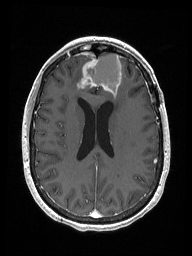
Brain MRI from a brain-tumour surgery series, one axial slice. Slice 69 of 192 in the series (ordered by position). T1-weighted post-contrast. 192 × 256 image matrix, field of view 187 × 250 mm. Case-level facts recorded for this patient, not image findings: histopathology: Metastastic Carcinoma from Breast primary; tumour location: Right Frontal.
Structures marked on this image (expert manual segmentation):
- previous resection cavity: bounding box (x1, y1, x2, y2) in pixels: (87, 53, 122, 95)